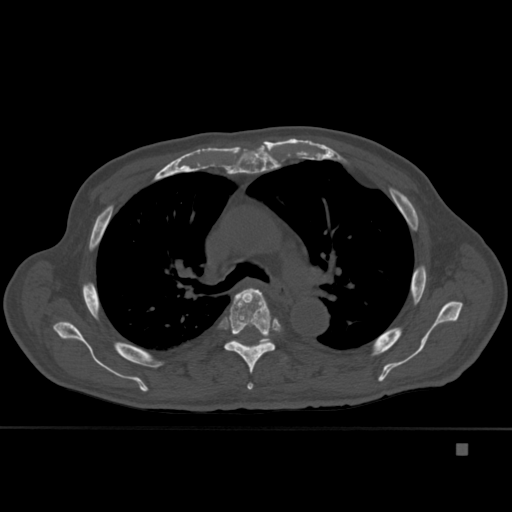
CT including the spine, one axial slice. Slice 307 of 451 in the series (ordered by position). Bone window (W 1800 / L 400 HU). 1.5 mm slice thickness. 512 × 512 image matrix, field of view 378 × 378 mm. Patient: male, 75 years. From the clinical record (not read from this slice): primary cancer: prostate.
Outlined on this slice (semi-automatically segmented with operator editing):
- T4 vertebra: box from (x=239, y=306) to (x=254, y=390) px
- T5 vertebra: (x=224, y=288)–(x=281, y=374)
- T6 vertebra: (x=255, y=339)–(x=269, y=345)